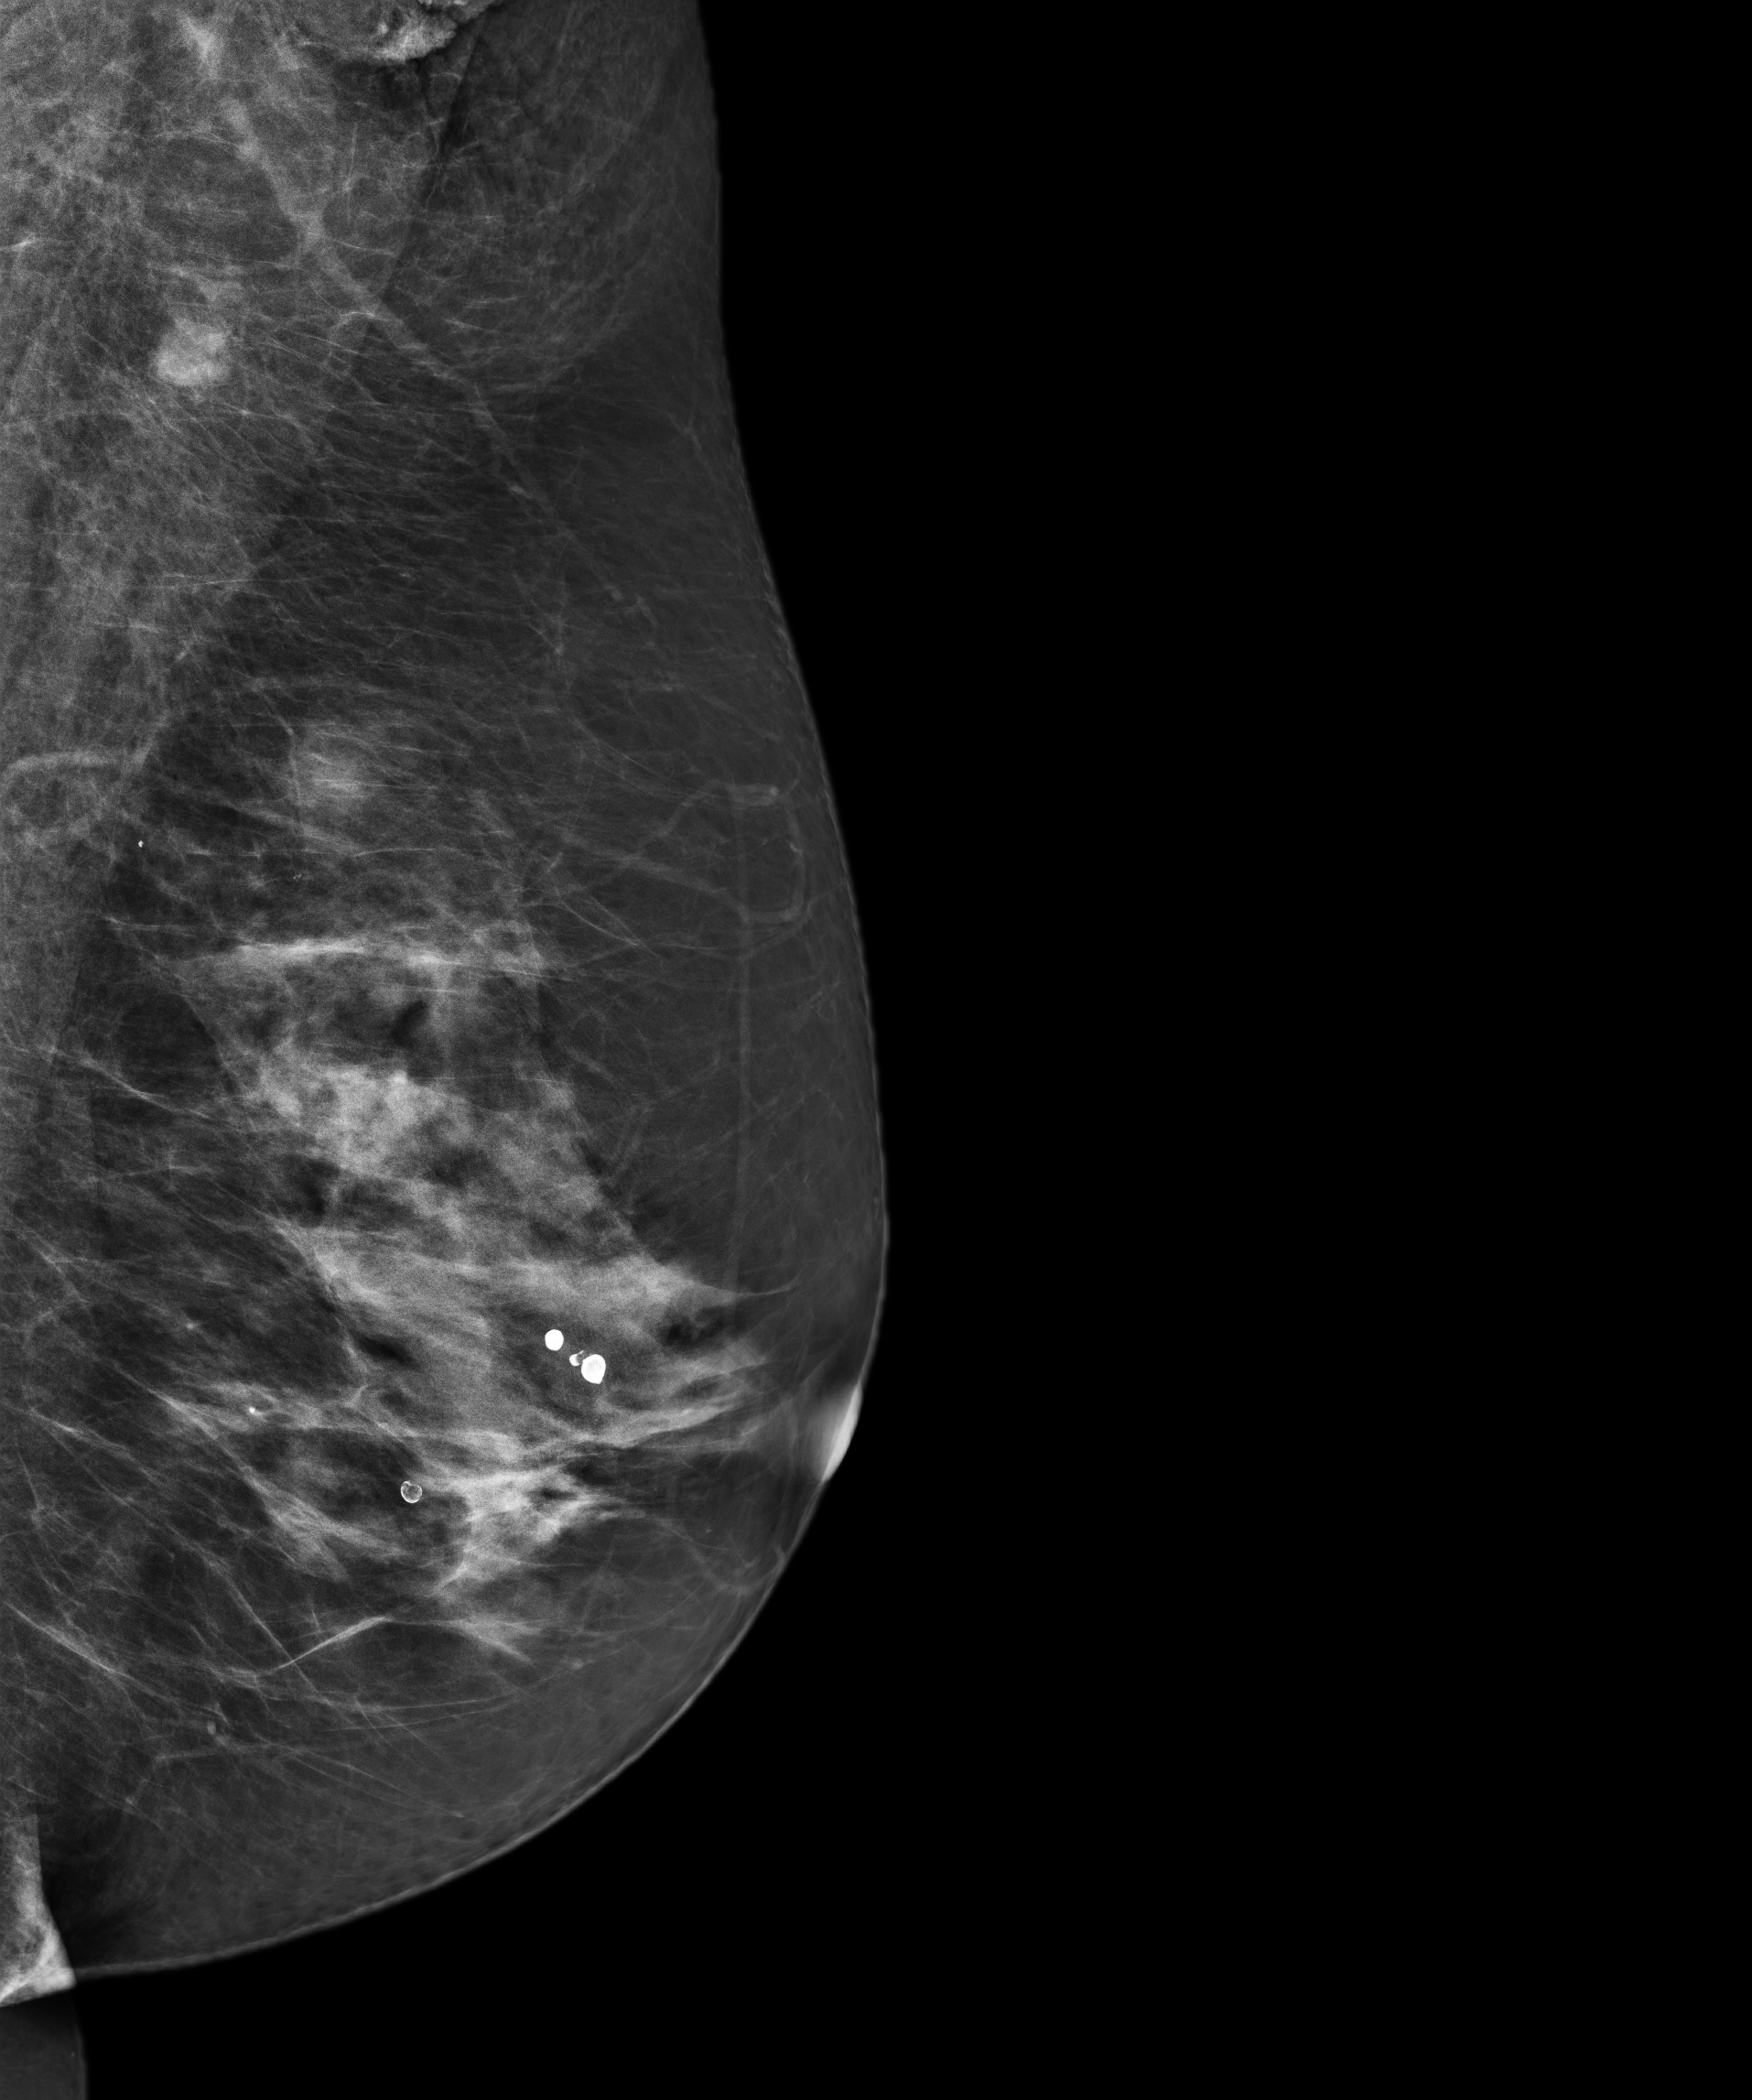
Annual screening mammography examination.
Image type: full-field digital mammogram. Breast: left. Projection: mediolateral oblique (MLO) view.